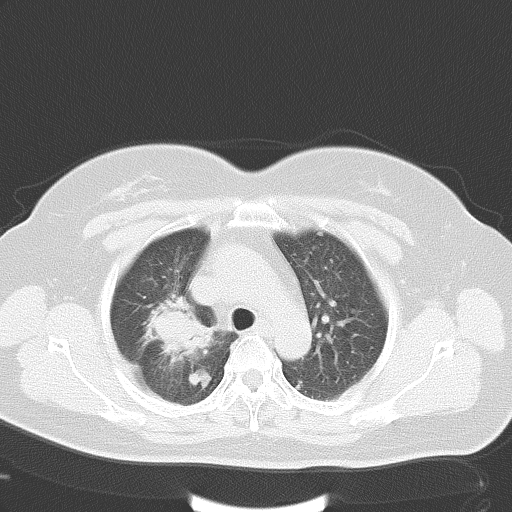
Chest CT, one axial slice. Slice 37 of 48 in the series (ordered by position). 120 kVp. Lung window (W 1500 / L -600 HU). 512 × 512 image matrix, field of view 353 × 353 mm. Female patient, age 50 years. Case-level facts recorded for this patient, not image findings: clinical TNM (as recorded): T2a N0 M1a.
Structures marked on this image (rectangle marked by the reading radiologist):
- lung tumour (recorded histology: adenocarcinoma): box from (x=138, y=291) to (x=221, y=363) px